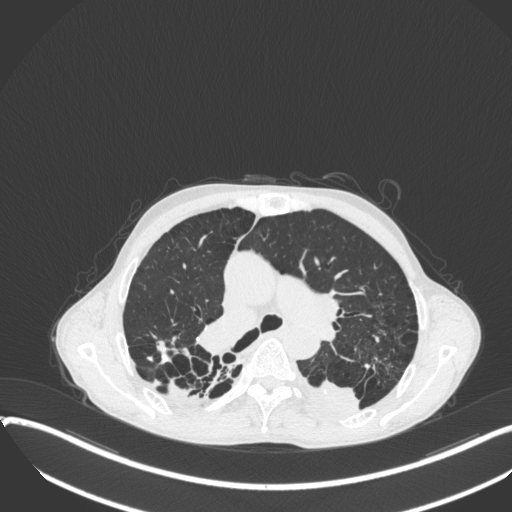
Chest CT, one axial slice; position 249 of 400 along the scan axis; reconstruction kernel B31f; lung window (W 1500 / L -600 HU); 1 mm slice thickness; 512 × 512 image matrix, field of view 400 × 400 mm. Male patient, age 57 years. From the clinical record (not read from this slice): clinical TNM (as recorded): T4 N0 M0.
Annotated regions visible in this slice (rectangle marked by the reading radiologist):
- lung tumour (recorded histology: squamous cell carcinoma): bounding box <304,375,362,415> (left, top, right, bottom; pixels)